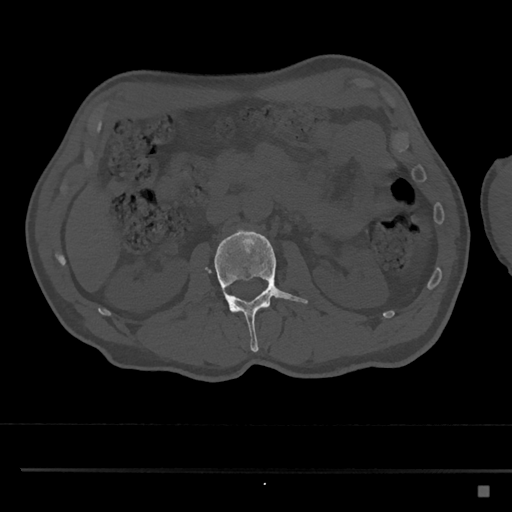
CT including the spine, one axial slice; slice 755 of 797 in the series (ordered by position); reconstruction kernel Br40s/3; bone window (W 1800 / L 400 HU); 512 × 512 image matrix. Male patient, age 59 years. From the clinical record (not read from this slice): primary cancer: prostate.
Annotated regions visible in this slice (semi-automatically segmented with operator editing):
- L2 vertebra: bounding box (x1, y1, x2, y2) in pixels: (205, 228, 308, 352)